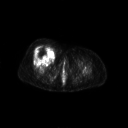
FDG PET of an extremity soft-tissue mass (from a PET/CT study), one axial slice. Slice 51 of 267 in the series (ordered by position). 3.27 mm slice thickness. 128 × 128 image matrix, field of view 700 × 700 mm. Female patient, age 56 years. Case-level facts recorded for this patient, not image findings: histological type: malignant solitary fibrous tumor; grade: intermediate; site of the primary tumour: right thigh.
Annotated regions visible in this slice (expert contour drawn on MRI and transferred to this co-registered scan by the dataset authors):
- gross tumour volume including surrounding oedema: box from (x=31, y=45) to (x=55, y=62) px
- gross tumour volume (mass): (x=32, y=45)–(x=54, y=62)